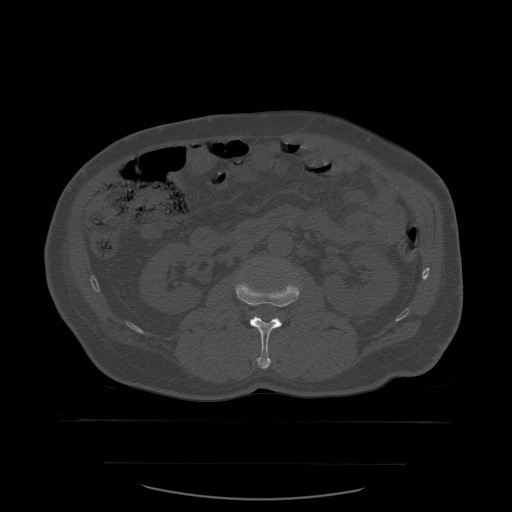
CT including the spine, one axial slice; slice 213 of 590 in the series (ordered by position); bone window (W 1800 / L 400 HU); 512 × 512 image matrix. Patient age 71 years. Case-level facts recorded for this patient, not image findings: primary cancer: lung.
Structures marked on this image (semi-automatically segmented with operator editing):
- L2 vertebra: bounding box <235,282,302,369> (left, top, right, bottom; pixels)